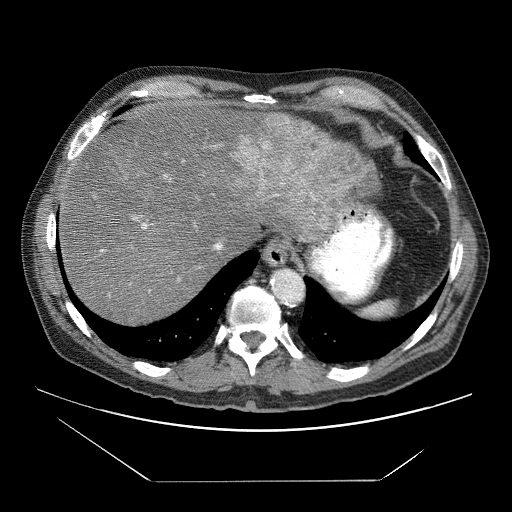
Contrast-enhanced abdominal CT (liver protocol), one axial slice; slice 58 of 83 in the series (ordered by position); 120 kVp; soft-tissue window (W 400 / L 40 HU); 512 × 512 image matrix. From the clinical record (not read from this slice): diagnosis: hepatocellular carcinoma (patient treated with transarterial chemoembolisation; whether this scan precedes or follows treatment is not stated here); TNM stage (as recorded): Stage-IVB; Child-Pugh class: B; tumour nodularity: uninodular.
Structures marked on this image (semi-automatically segmented with operator editing):
- liver parenchyma outside the tumour (the mass and vessels are separate outlines, so this box may not span the whole liver): bounding box (x1, y1, x2, y2) in pixels: (58, 92, 378, 324)
- mass: (237, 114, 374, 237)
- liver vessels: (100, 92, 342, 296)